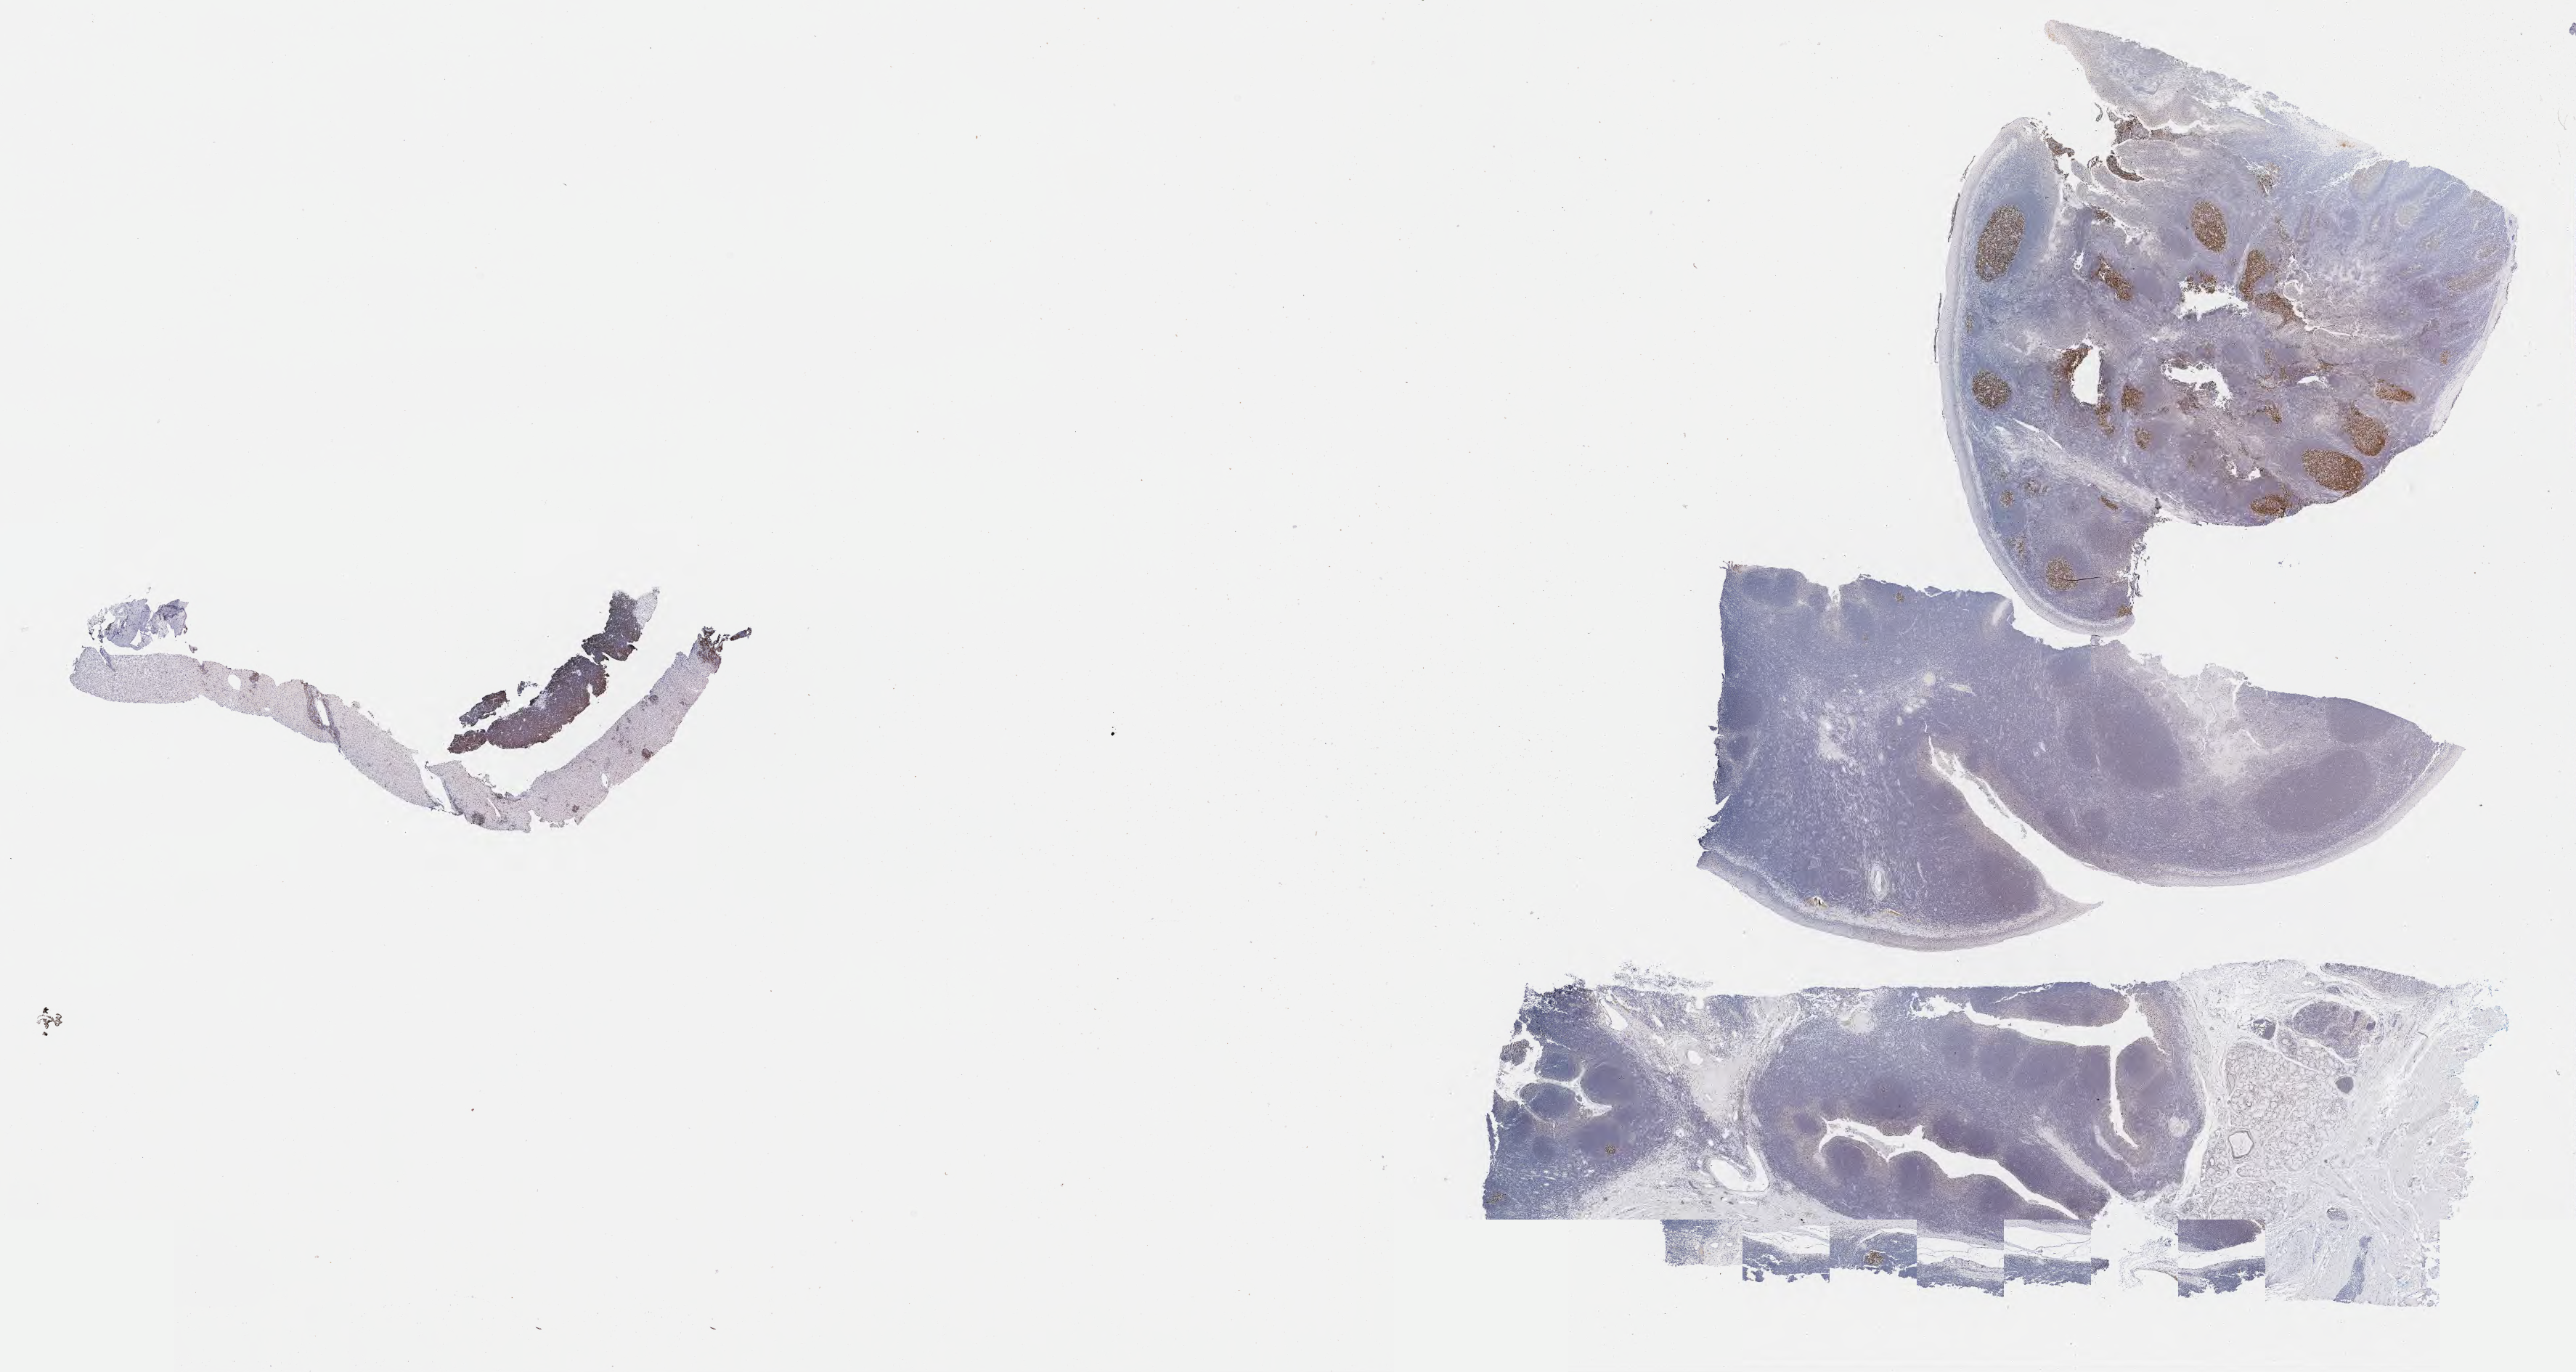
Whole-slide image, immunohistochemical stain for BCL6, low-resolution overview of the scanned area, about 28.7 x 15.3 mm; tumor tissue; site: liver. Male, age 7 years at initial diagnosis.
Histologic diagnosis: Burkitt lymphoma, NOS.